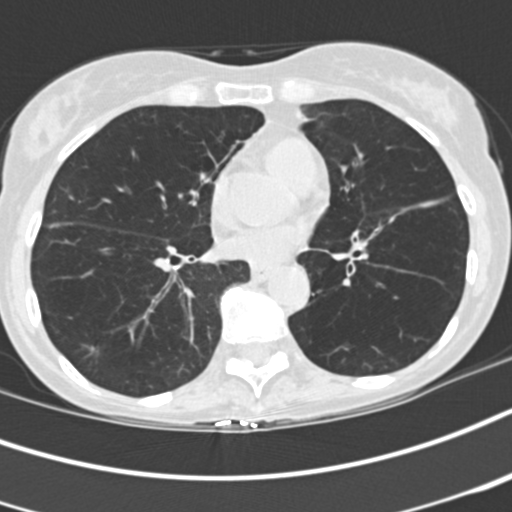
Low-dose screening chest CT, axial slice, first (baseline) screen, lung window (W 1500 / L -600 HU), 2 mm slice thickness, standard (soft-tissue) reconstruction kernel (B30f), 512 × 512 image matrix. Female, age 68 years at enrolment. Former smoker at enrolment.
- Expert-annotated lung lesion, box from (x=71, y=335) to (x=113, y=366) px.
- Screening reader's record for this exam (one nodule recorded; not confirmed to be the boxed lesion): non-calcified nodule or mass ≥4 mm, right lower lobe, 8 × 4 mm, spiculated (stellate) margins, soft tissue attenuation.
- Participant outcome: lung cancer diagnosed 1012 days after this screen — squamous cell carcinoma, NOS, right lower lobe, stage IA (AJCC 6th edition).